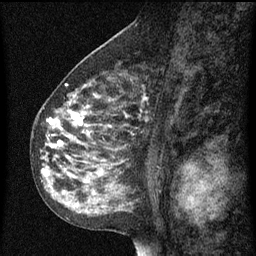
Breast MRI (dynamic contrast-enhanced), one sagittal slice; position 41 of 60 along the scan axis; dynamic contrast-enhanced series, image 2 of 3 at this slice position (ordered by acquisition); 1.5 T; TE 4.2 ms, TR 8 ms; 2 mm slice thickness; 256 × 256 image matrix, field of view 180 × 180 mm. Female patient, age 55 years.
Structures marked on this image (semi-automatic segmentation, software-assisted and operator-edited):
- analysis volume of interest (the breast-tissue region the enhancement analysis was run in; not a lesion): bounding box (x1, y1, x2, y2) in pixels: (34, 68, 155, 151)
- tumour enhancement mask (voxels above the 70 % enhancement threshold inside the analysis volume of interest): (48, 84, 149, 149)